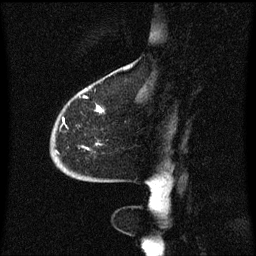
Breast MRI (dynamic contrast-enhanced), one sagittal slice. Position 17 of 60 along the scan axis. Dynamic contrast-enhanced series, image 2 of 3 at this slice position (ordered by acquisition). 1.5 T. TE 4.2 ms, TR 8.4 ms. 256 × 256 image matrix, field of view 200 × 200 mm. Patient: female, 68 years. From the clinical record (not read from this slice): setting: breast cancer imaged before/during neoadjuvant chemotherapy; receptor status: triple-negative.
Structures marked on this image (semi-automatic segmentation, software-assisted and operator-edited):
- analysis volume of interest (the breast-tissue region the enhancement analysis was run in; not a lesion): box from (x=52, y=94) to (x=106, y=173) px
- tumour enhancement mask (voxels above the 70 % enhancement threshold inside the analysis volume of interest): (x=97, y=106)–(x=105, y=113)